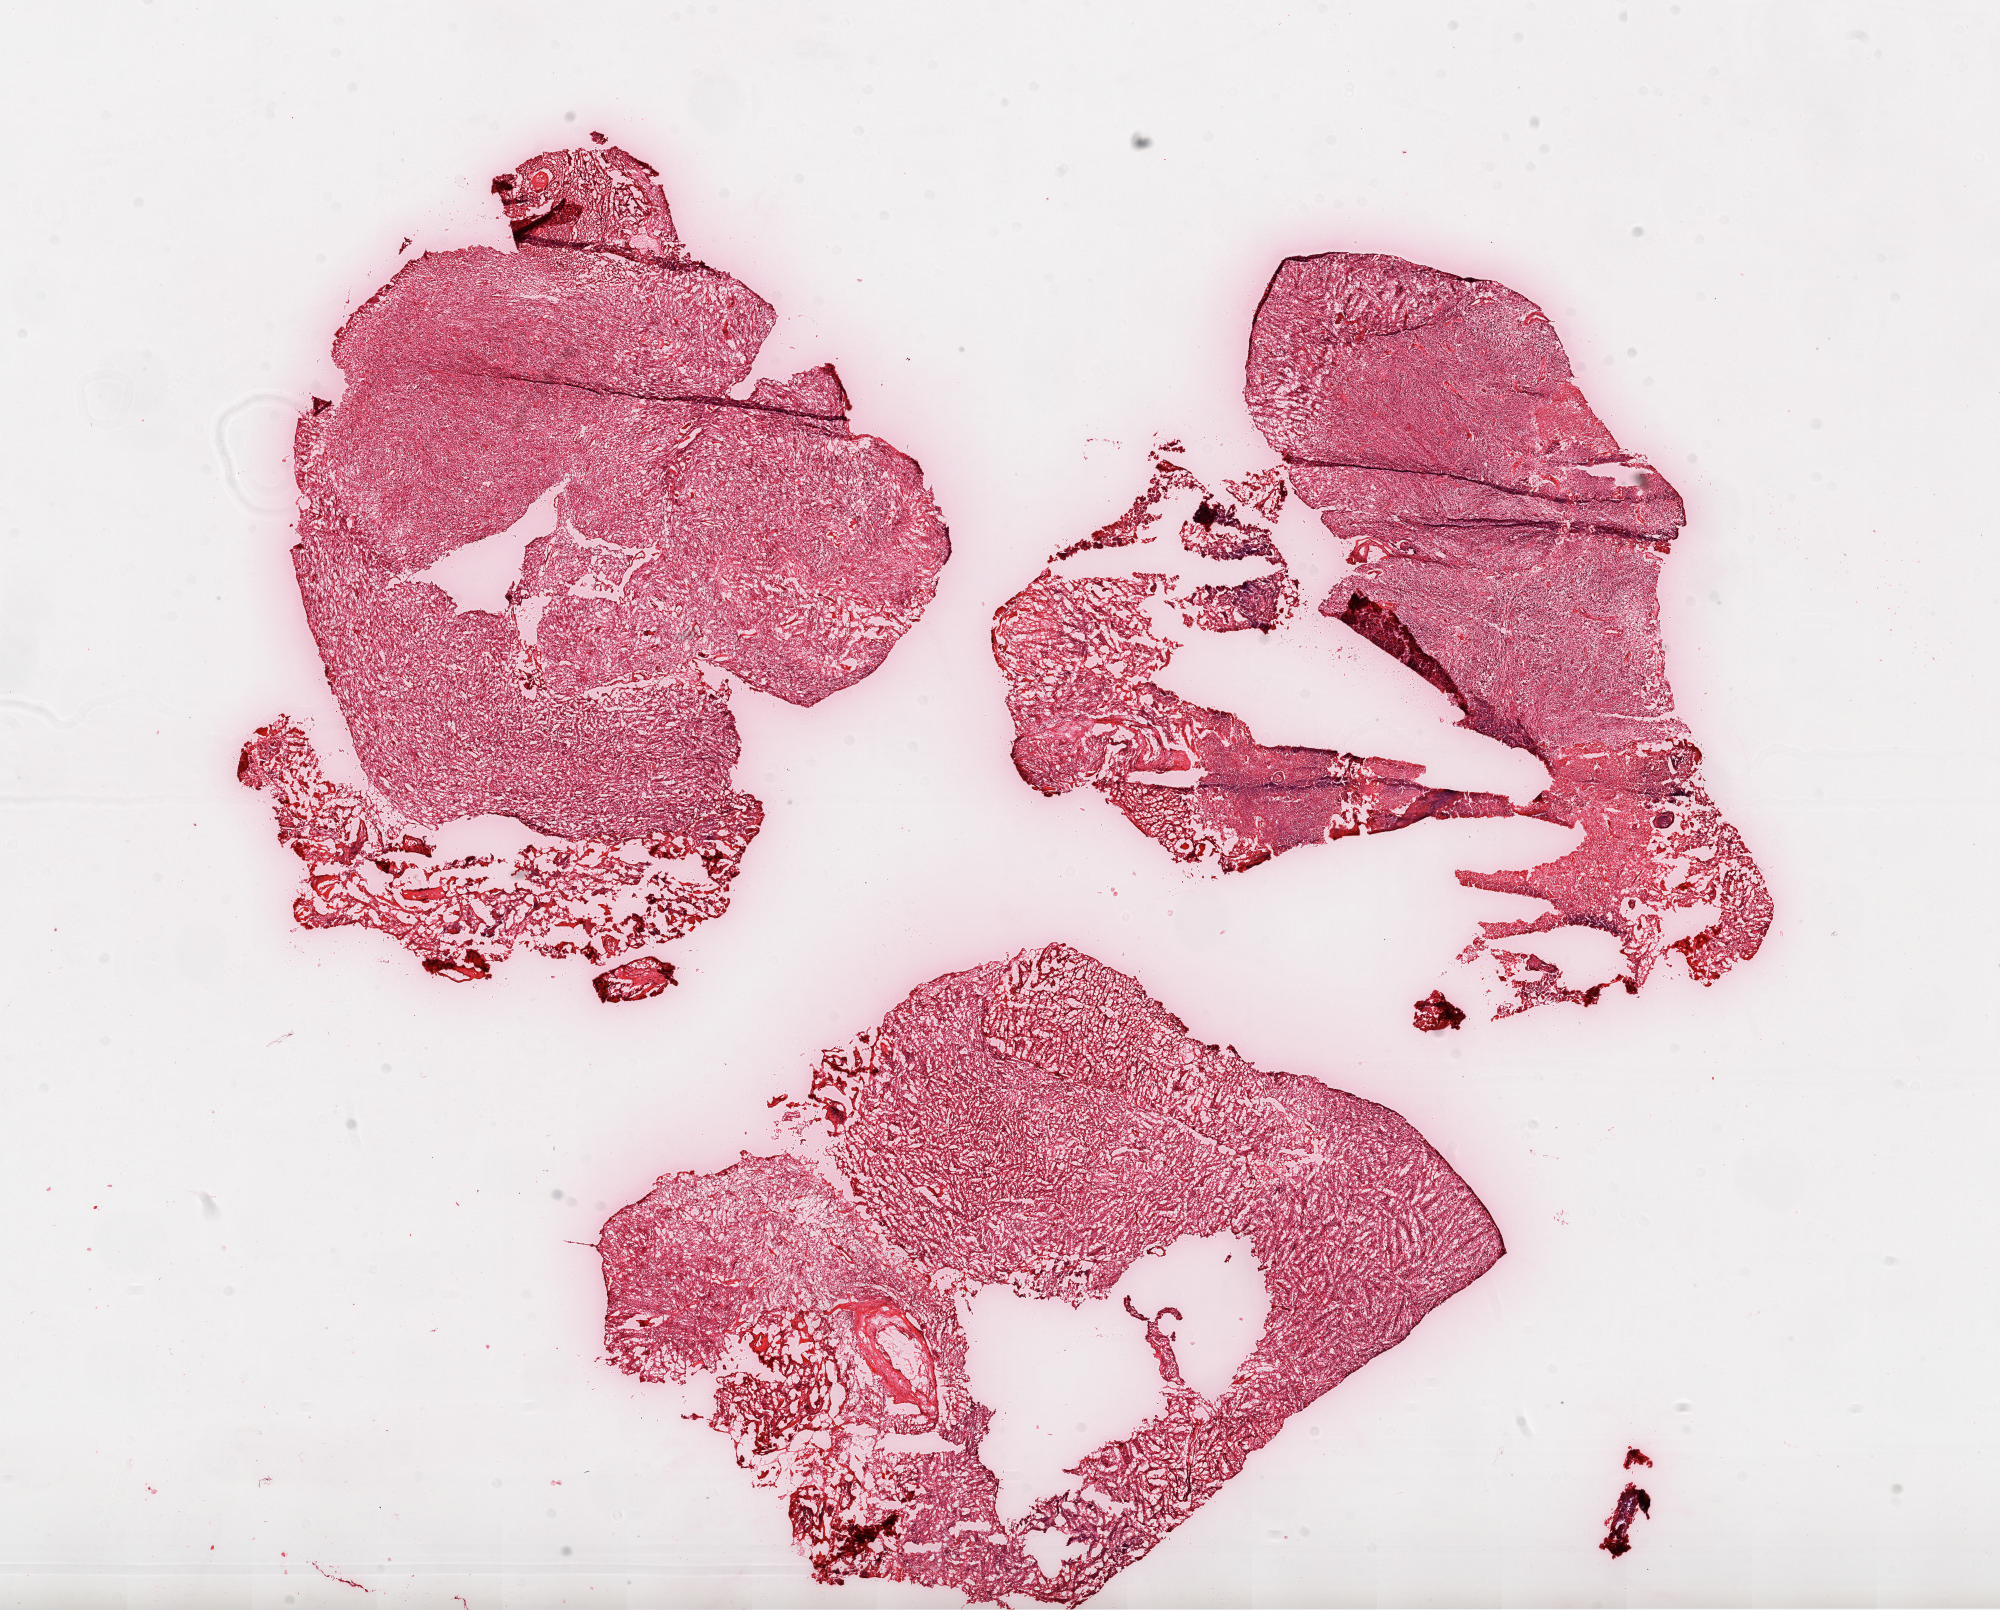
Digitized H&E tissue section (whole slide) — low-resolution overview of the scanned area, about 16.0 x 12.9 mm; frozen section; primary tumour sample from the brain. Female, age 58 years at initial diagnosis. Composition of this section per pathologist review: tumour cells 85%, tumour nuclei 95%, stromal cells 5%, necrosis 10%.
• histologic diagnosis: Glioblastoma